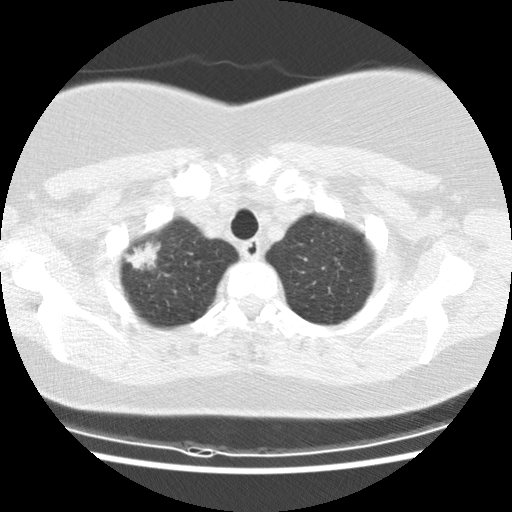
Low-dose screening chest CT, one axial slice. Reconstruction kernel STANDARD. 120 kVp. Lung window (W 1500 / L -600 HU). 512 × 512 image matrix, field of view 326 × 326 mm.
Outlined on this slice (outlined manually by an expert reader):
- lesion 1 (tumor, upper lobe of right lung): bounding box (x1, y1, x2, y2) in pixels: (128, 242, 161, 271)